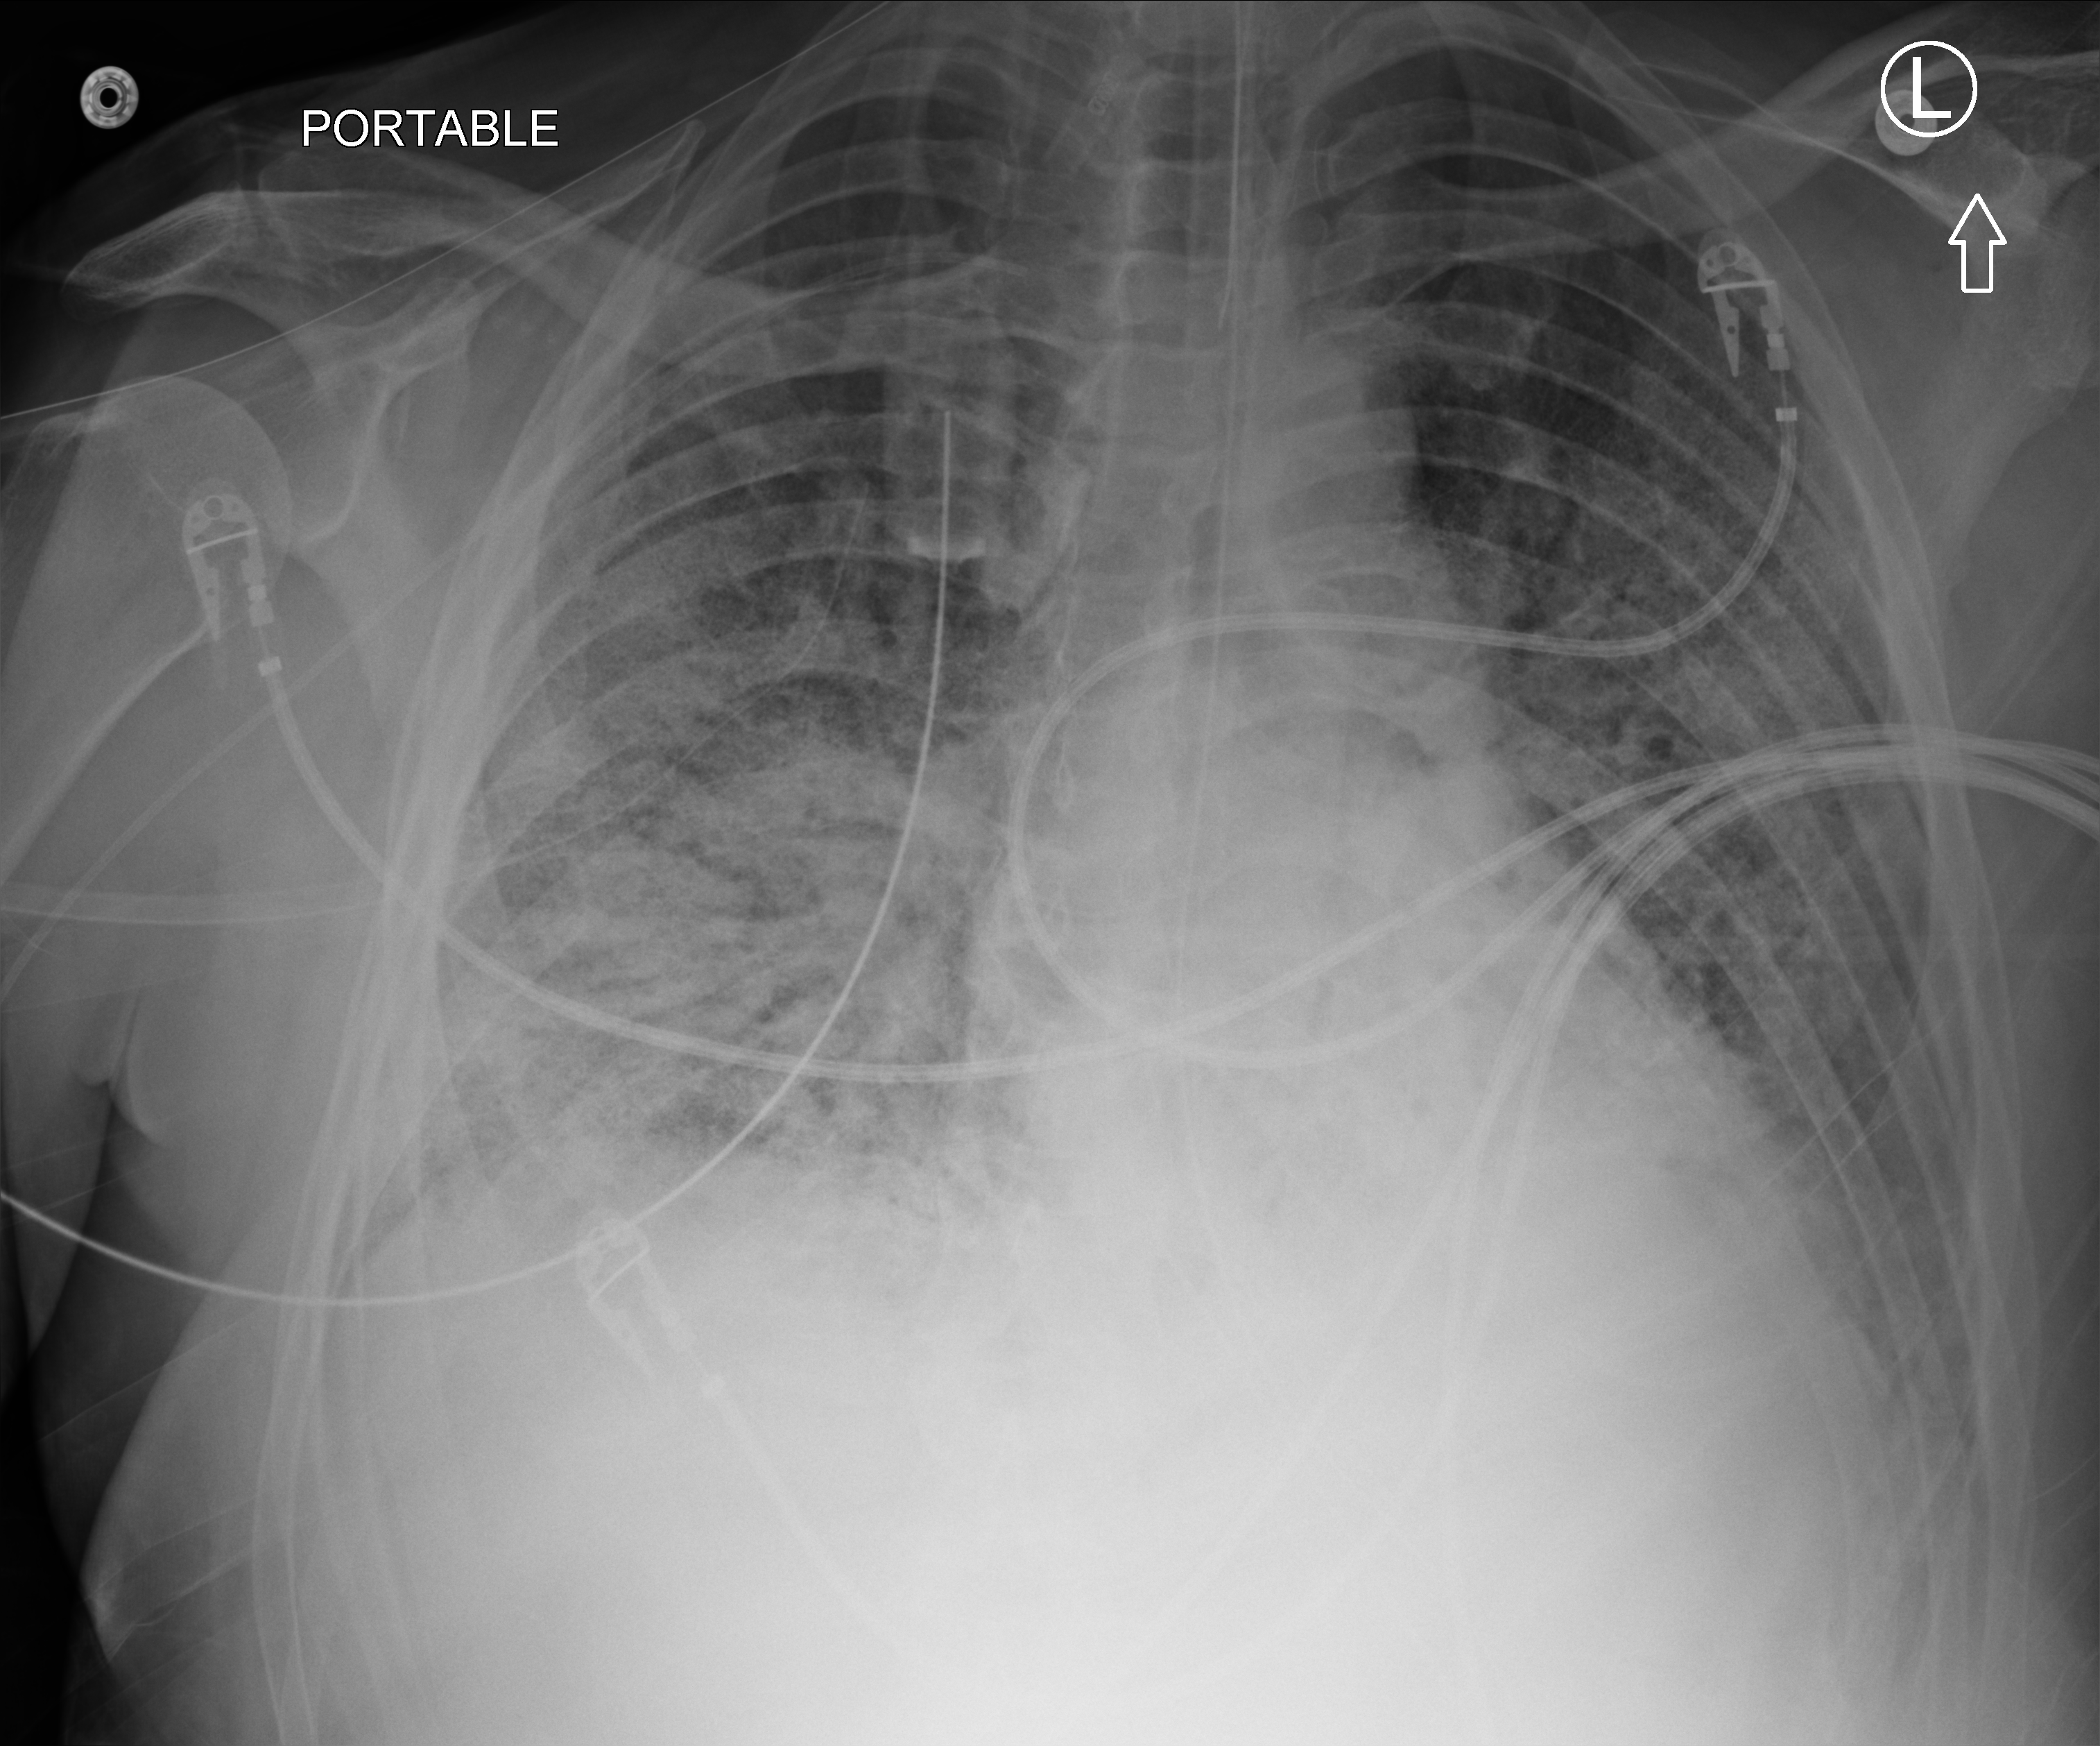
Portable chest radiograph; anteroposterior (AP) projection. Male patient hospitalised with COVID-19, age 18–59 years.
Hospital-stay facts (about this admission, not read from this image; timing relative to this image not recorded): mechanically ventilated during this hospital stay: yes; admitted to intensive care during this hospital stay: yes.